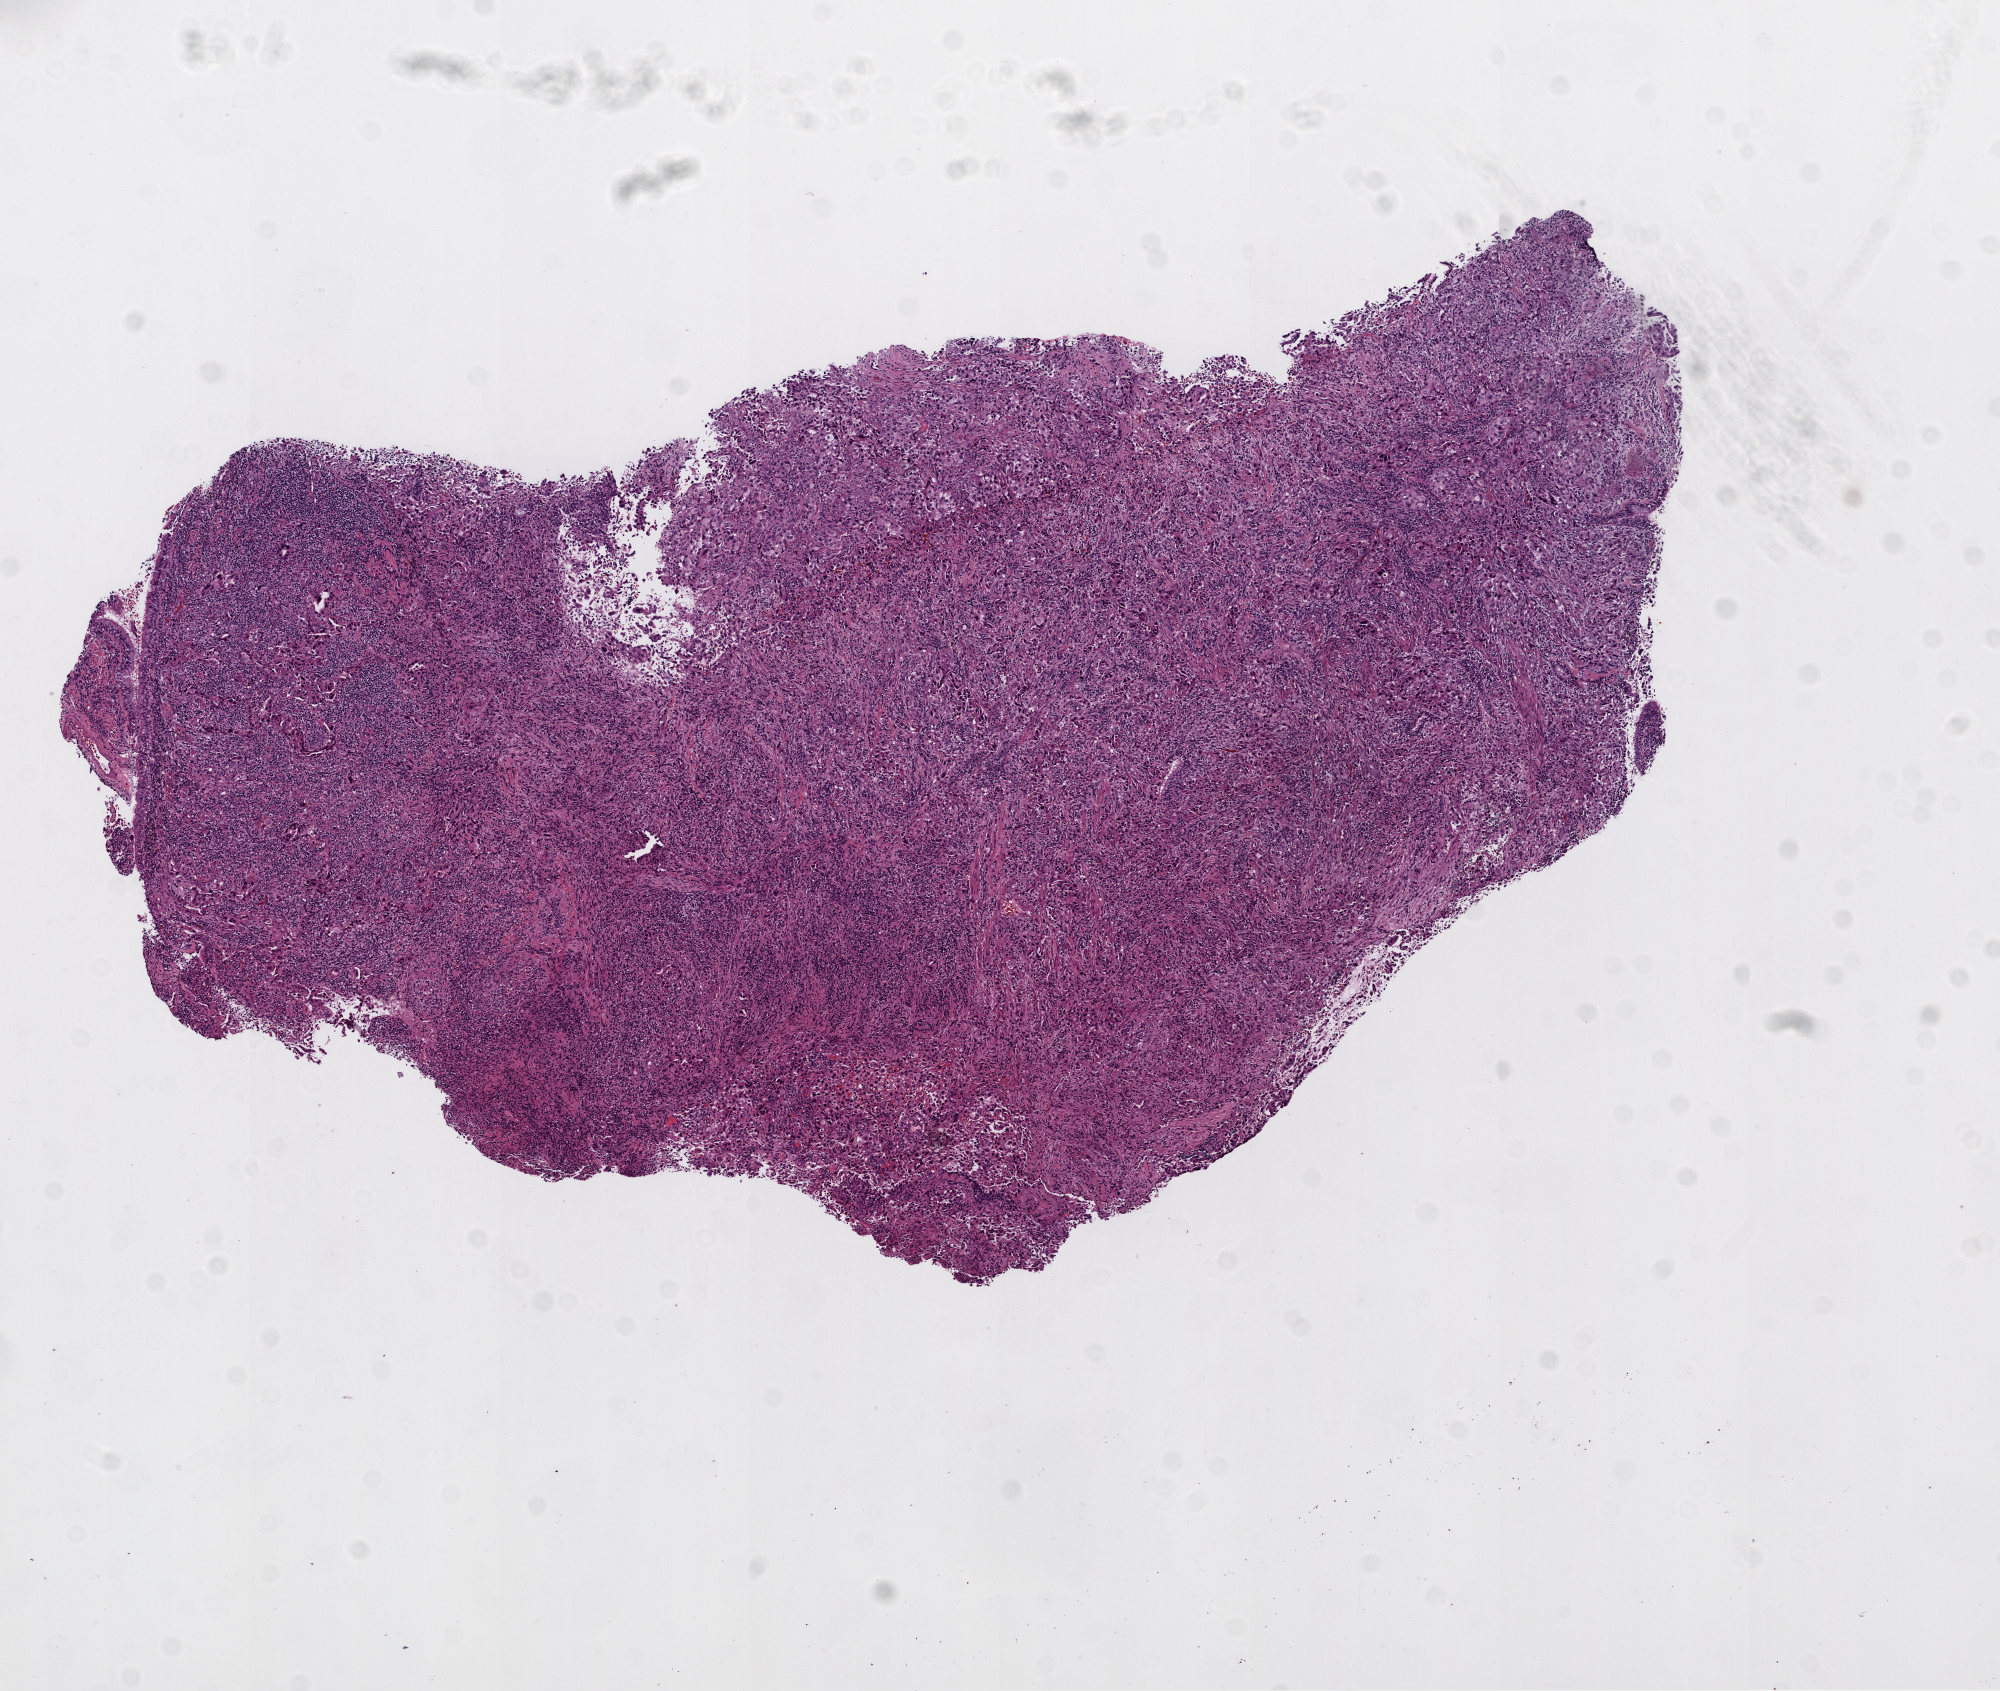
Whole-slide histology image, Hematoxylin and eosin (H&E) stained, low-resolution overview of the scanned area, about 8.0 x 6.8 mm (acquisition: 20x scan); frozen section from the top of the tissue portion; lung, primary tumour sample. Female patient; age at initial diagnosis 66 years.
Pathologic diagnosis: Adenocarcinoma, NOS.